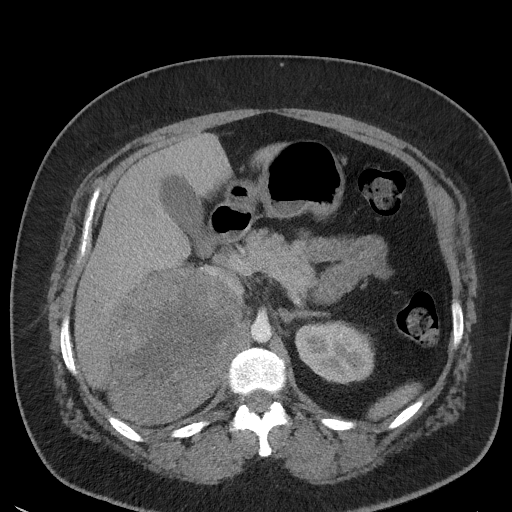
Contrast-enhanced abdominal CT, one axial slice; slice 31 of 56 in the series (ordered by position); reconstruction kernel I41f/3; 120 kVp; intravenous contrast given; soft-tissue window (W 400 / L 40 HU); 5 mm slice thickness; 512 × 512 image matrix, field of view 373 × 373 mm. Patient: female, 35 years. From the clinical record (not read from this slice): diagnosis: adrenocortical carcinoma; tumour side: right adrenal; tumour size at pathology: 15 cm; Ki-67 index: 40 %; stage (as recorded): 2.
Annotated regions visible in this slice (semi-automatic segmentation, software-assisted and operator-edited):
- mass: bounding box <111,273,239,422> (left, top, right, bottom; pixels)